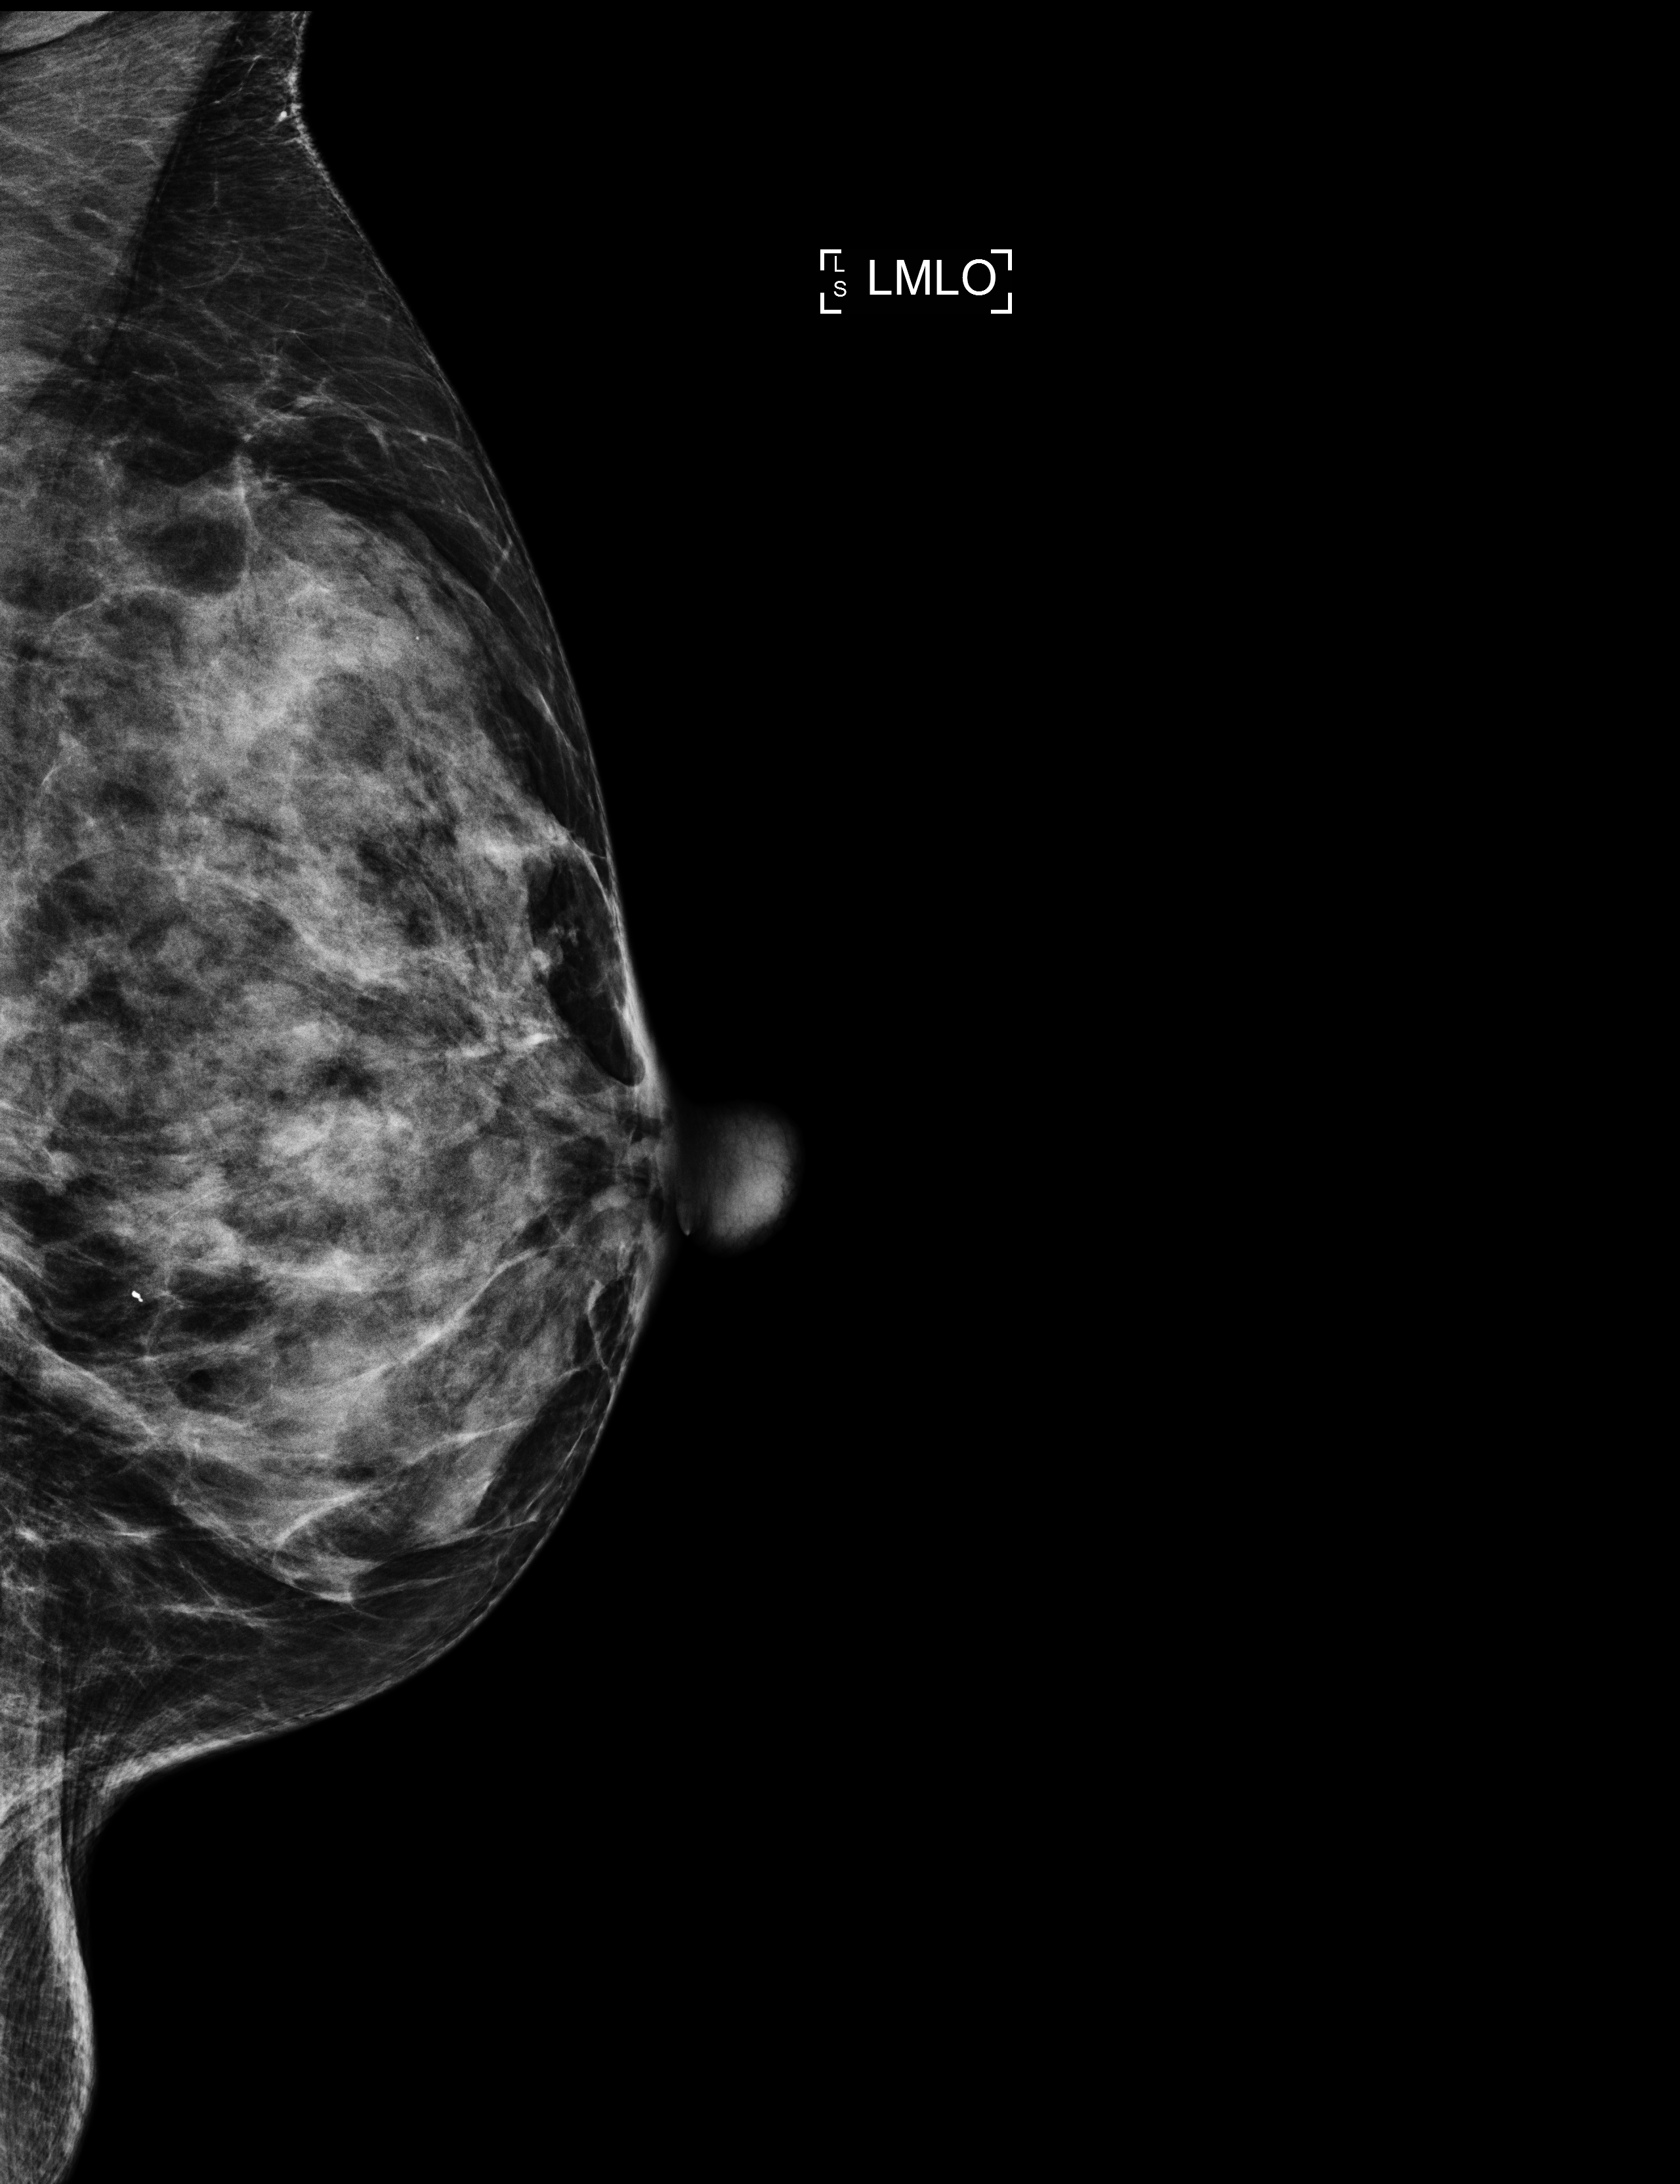
Digital mammogram (FFDM), left breast, mediolateral oblique (MLO) view, annual screening mammography examination, compressed breast thickness 41 mm. Patient aged 67 years (female).
- BI-RADS breast density category at the screening exam (both breasts, scale 1–4): 4
- final BI-RADS assessment for this screening round (tomosynthesis exam, both breasts): category 2
- recall: no recall after this screen